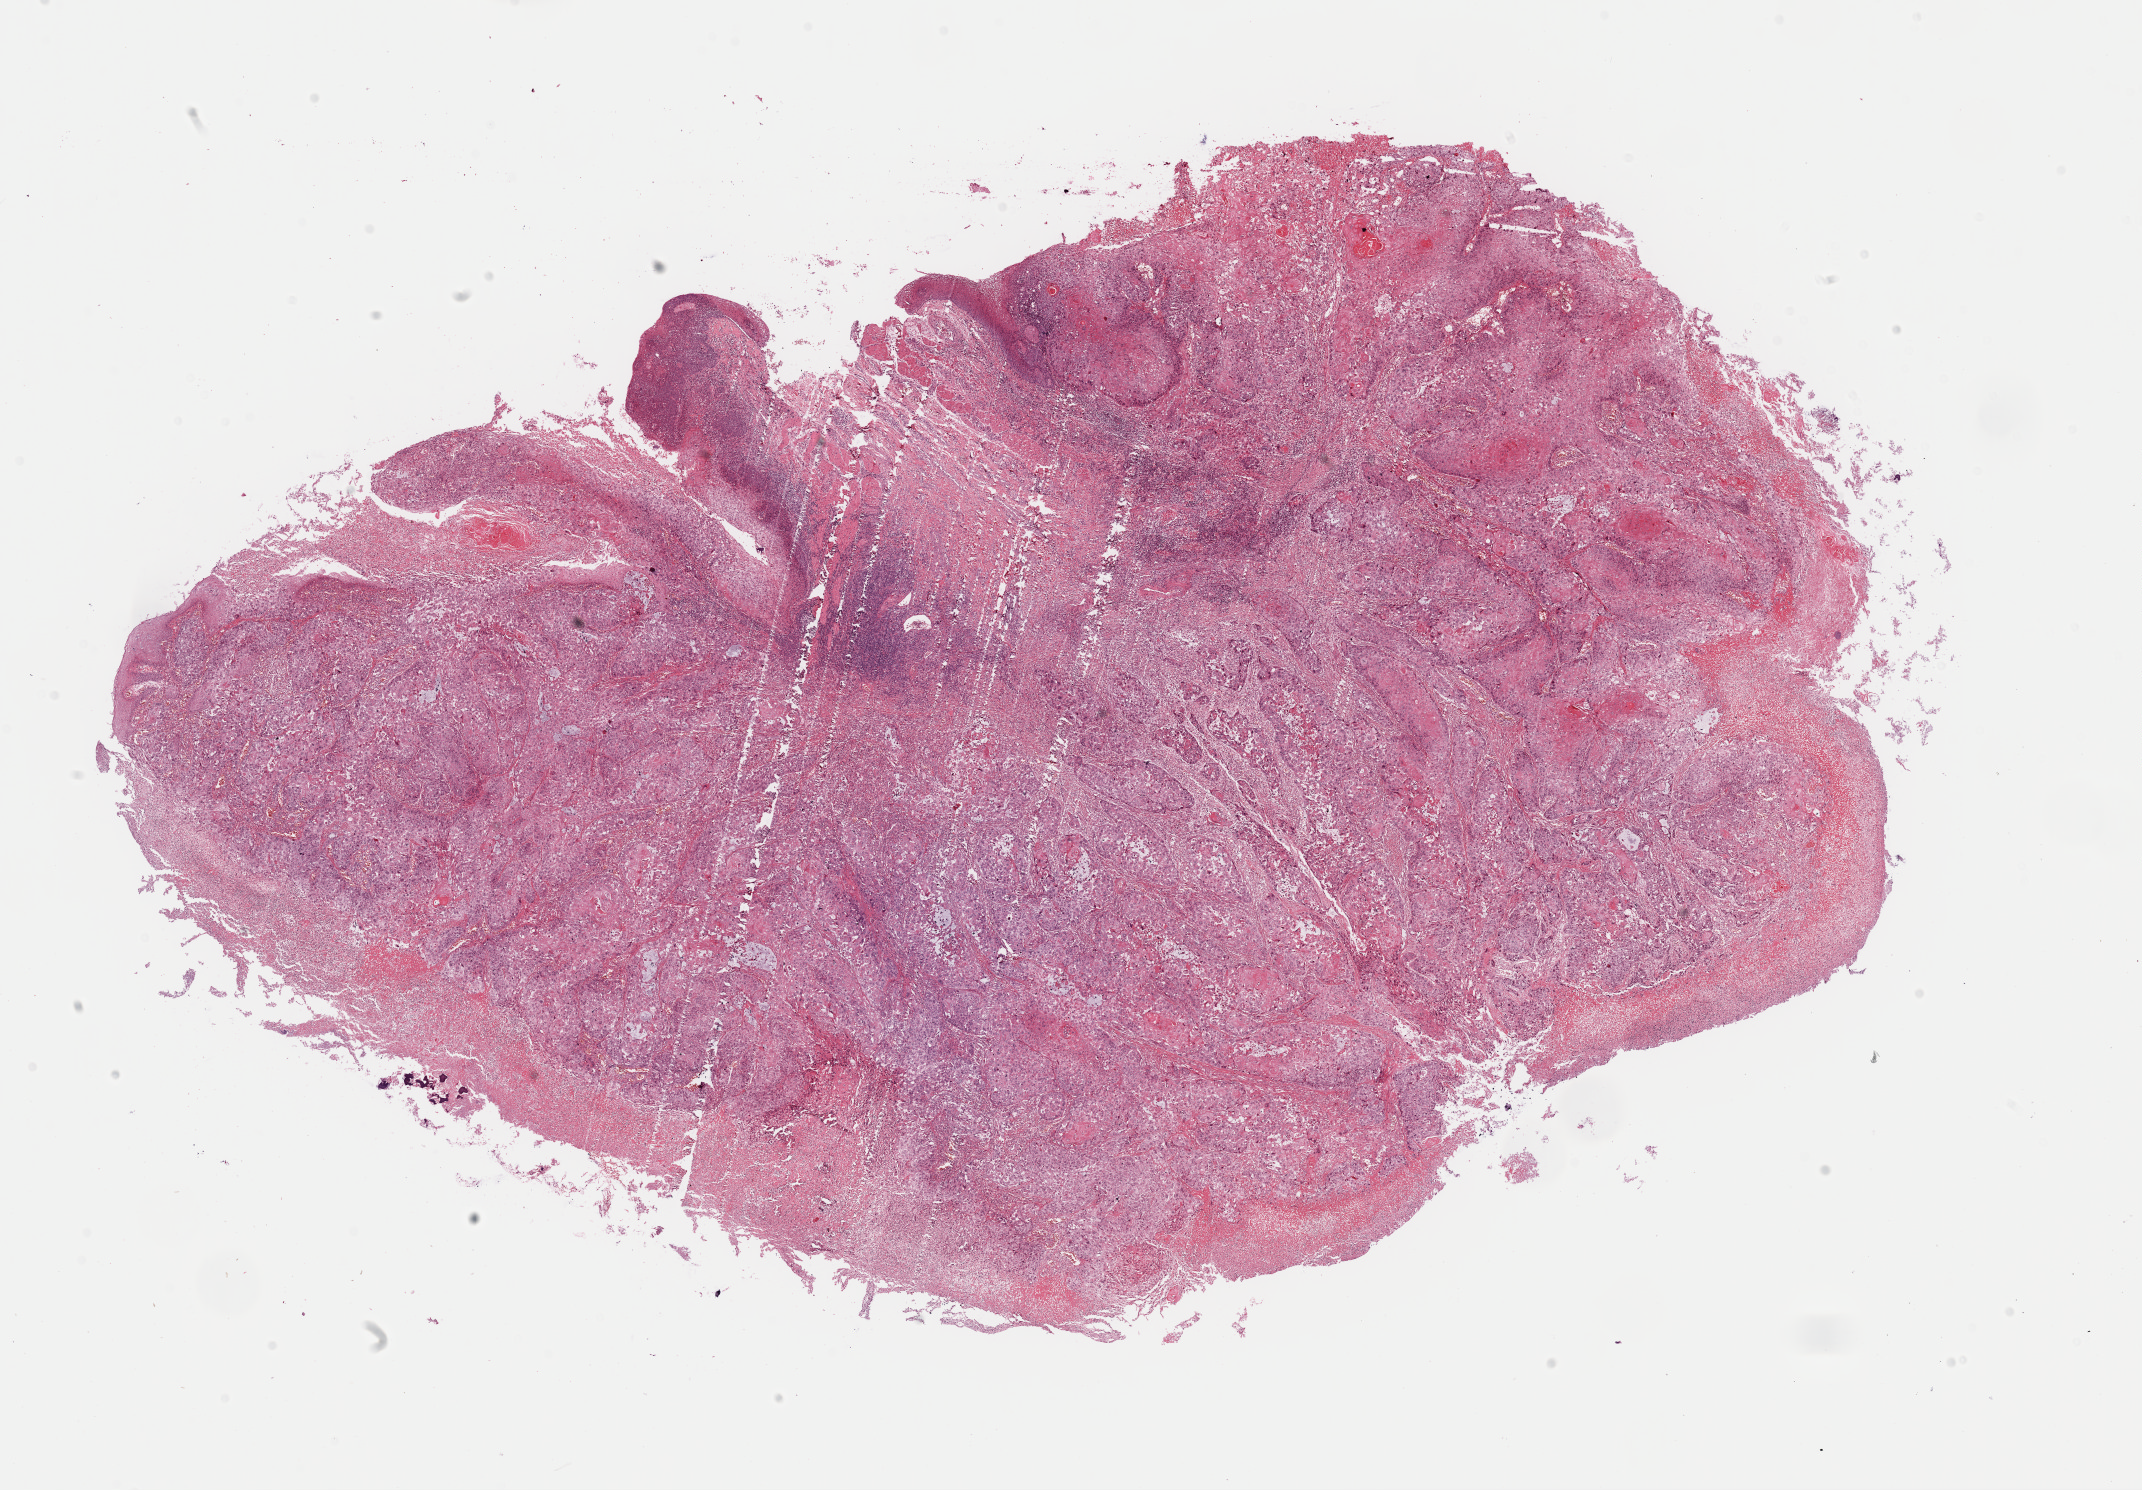
H&E whole-slide image — shown as a low-resolution overview of the whole scanned area (about 16.9 x 11.8 mm, from a 40x scan), FFPE section, primary tumour sample from the esophagus. Male, age 61 years at initial diagnosis. Histologic grade: G2 (moderately differentiated).
TNM: T3 N1 M0. Histologic diagnosis: Squamous cell carcinoma, NOS (middle third of esophagus). AJCC pathologic stage: III (6th edition).